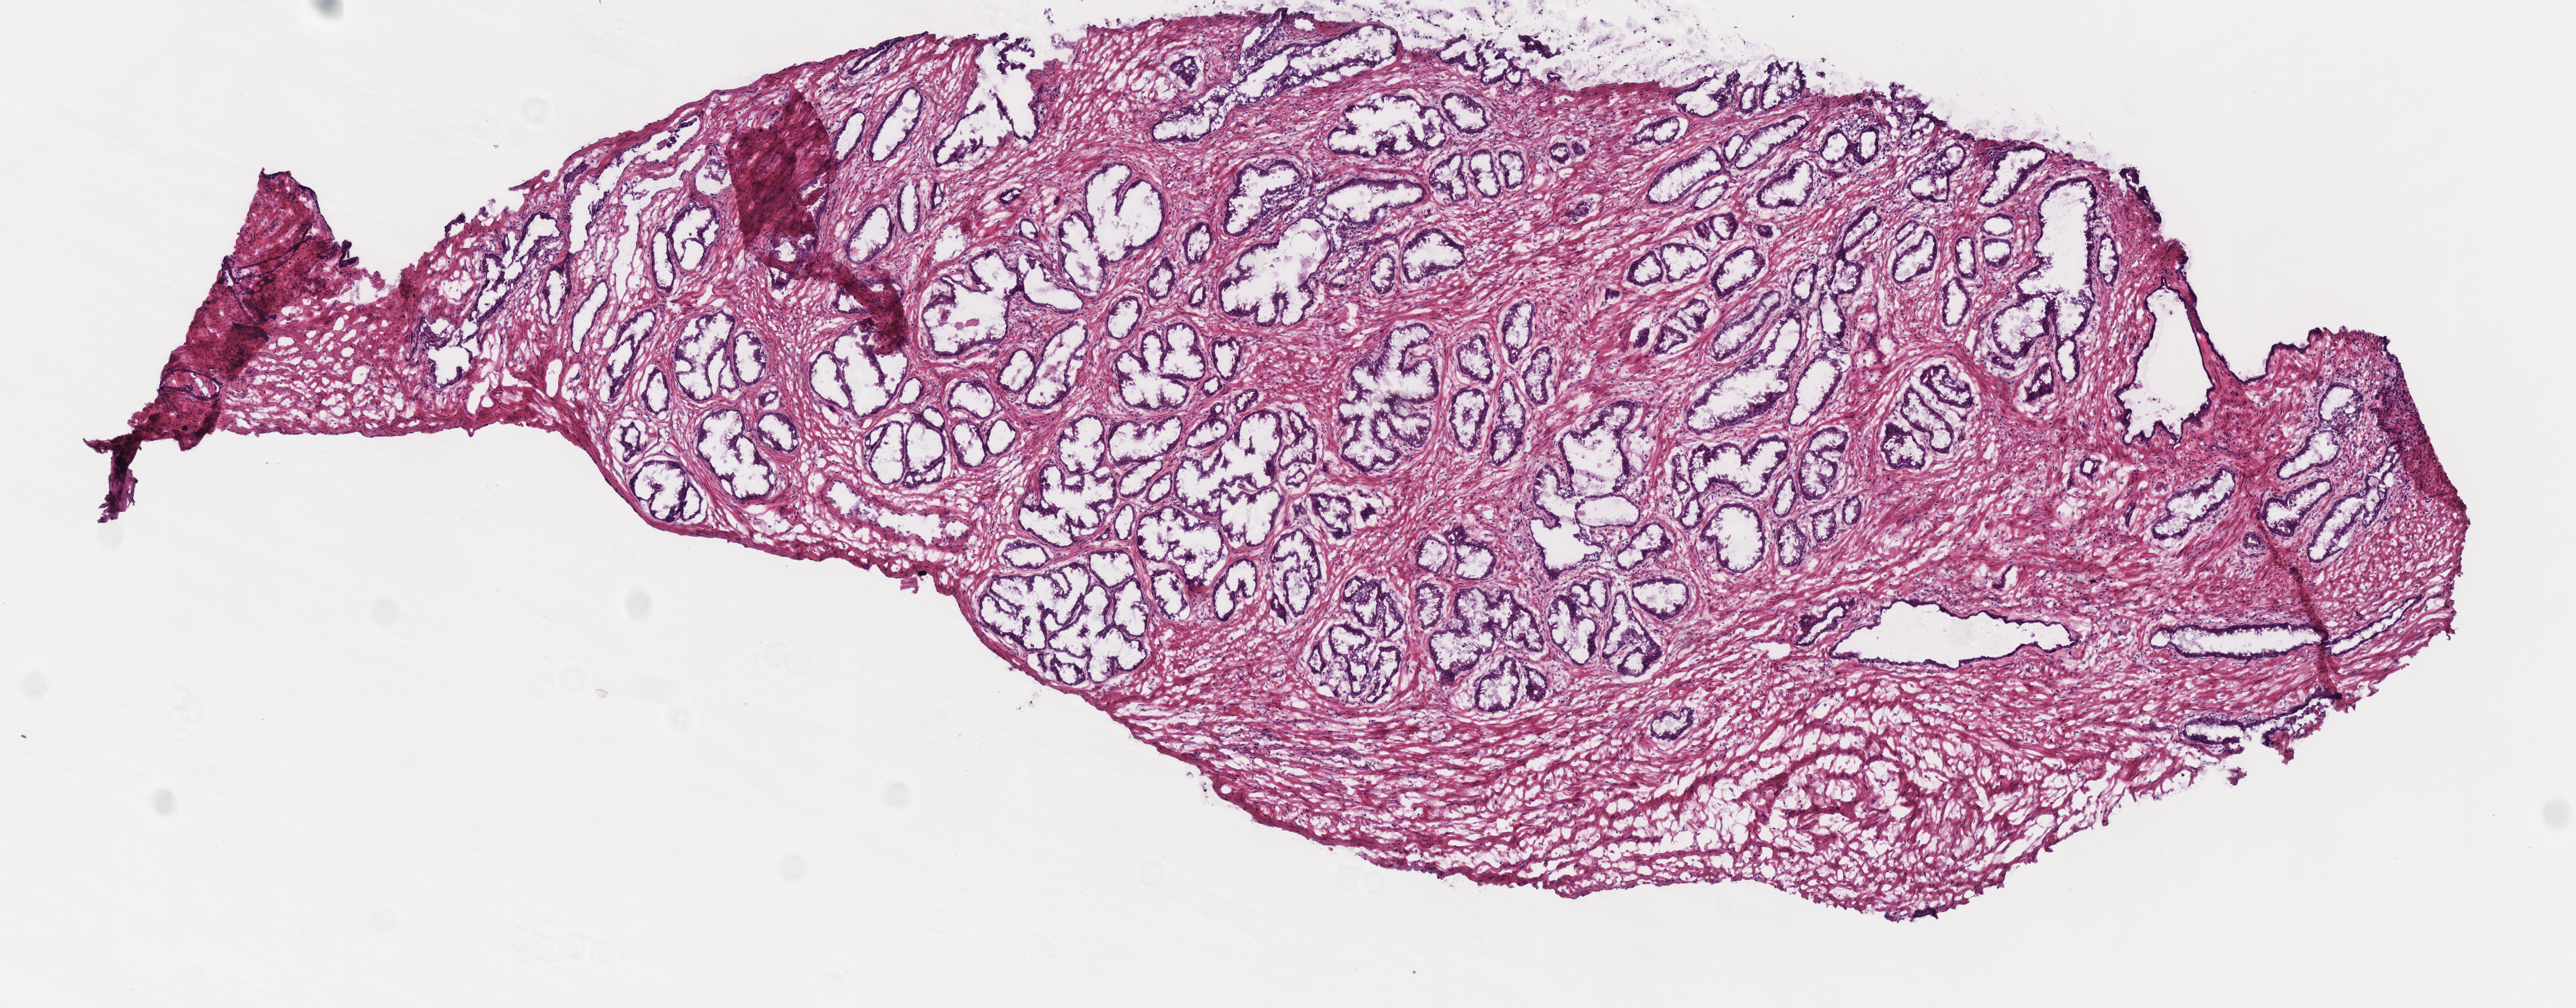
Digitized H&E tissue section (whole slide) — a low-resolution overview of the entire scanned area, about 7.3 x 2.9 mm (acquisition: 40x scan), frozen section from the top of the tissue portion, prostate, solid tissue normal (non-tumour tissue) sample. Male, age 61 years at initial diagnosis.
This section: solid tissue normal sample (biorepository sample class). Patient diagnosis: Acinar cell carcinoma (prostate gland).